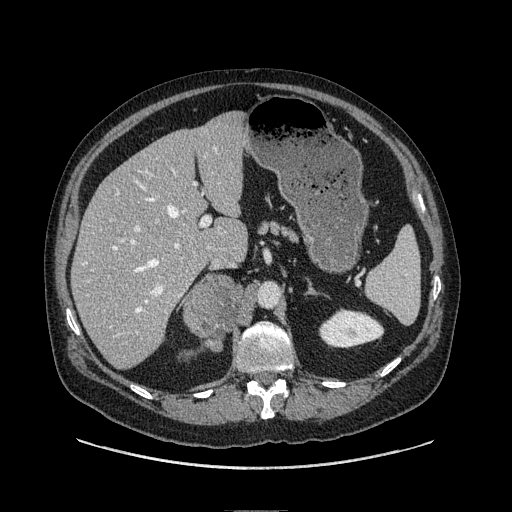
Contrast-enhanced abdominal CT, one axial slice. Slice 57 of 149 in the series (ordered by position). Soft-tissue window (W 400 / L 40 HU). 512 × 512 image matrix, field of view 440 × 440 mm. Male patient. From the clinical record (not read from this slice): diagnosis: adrenocortical carcinoma; tumour side: right adrenal; tumour size at pathology: 7.5 cm; Ki-67 index: 15 %; stage (as recorded): 2.
Outlined on this slice (semi-automatic segmentation, software-assisted and operator-edited):
- mass: bounding box (x1, y1, x2, y2) in pixels: (185, 273, 243, 349)